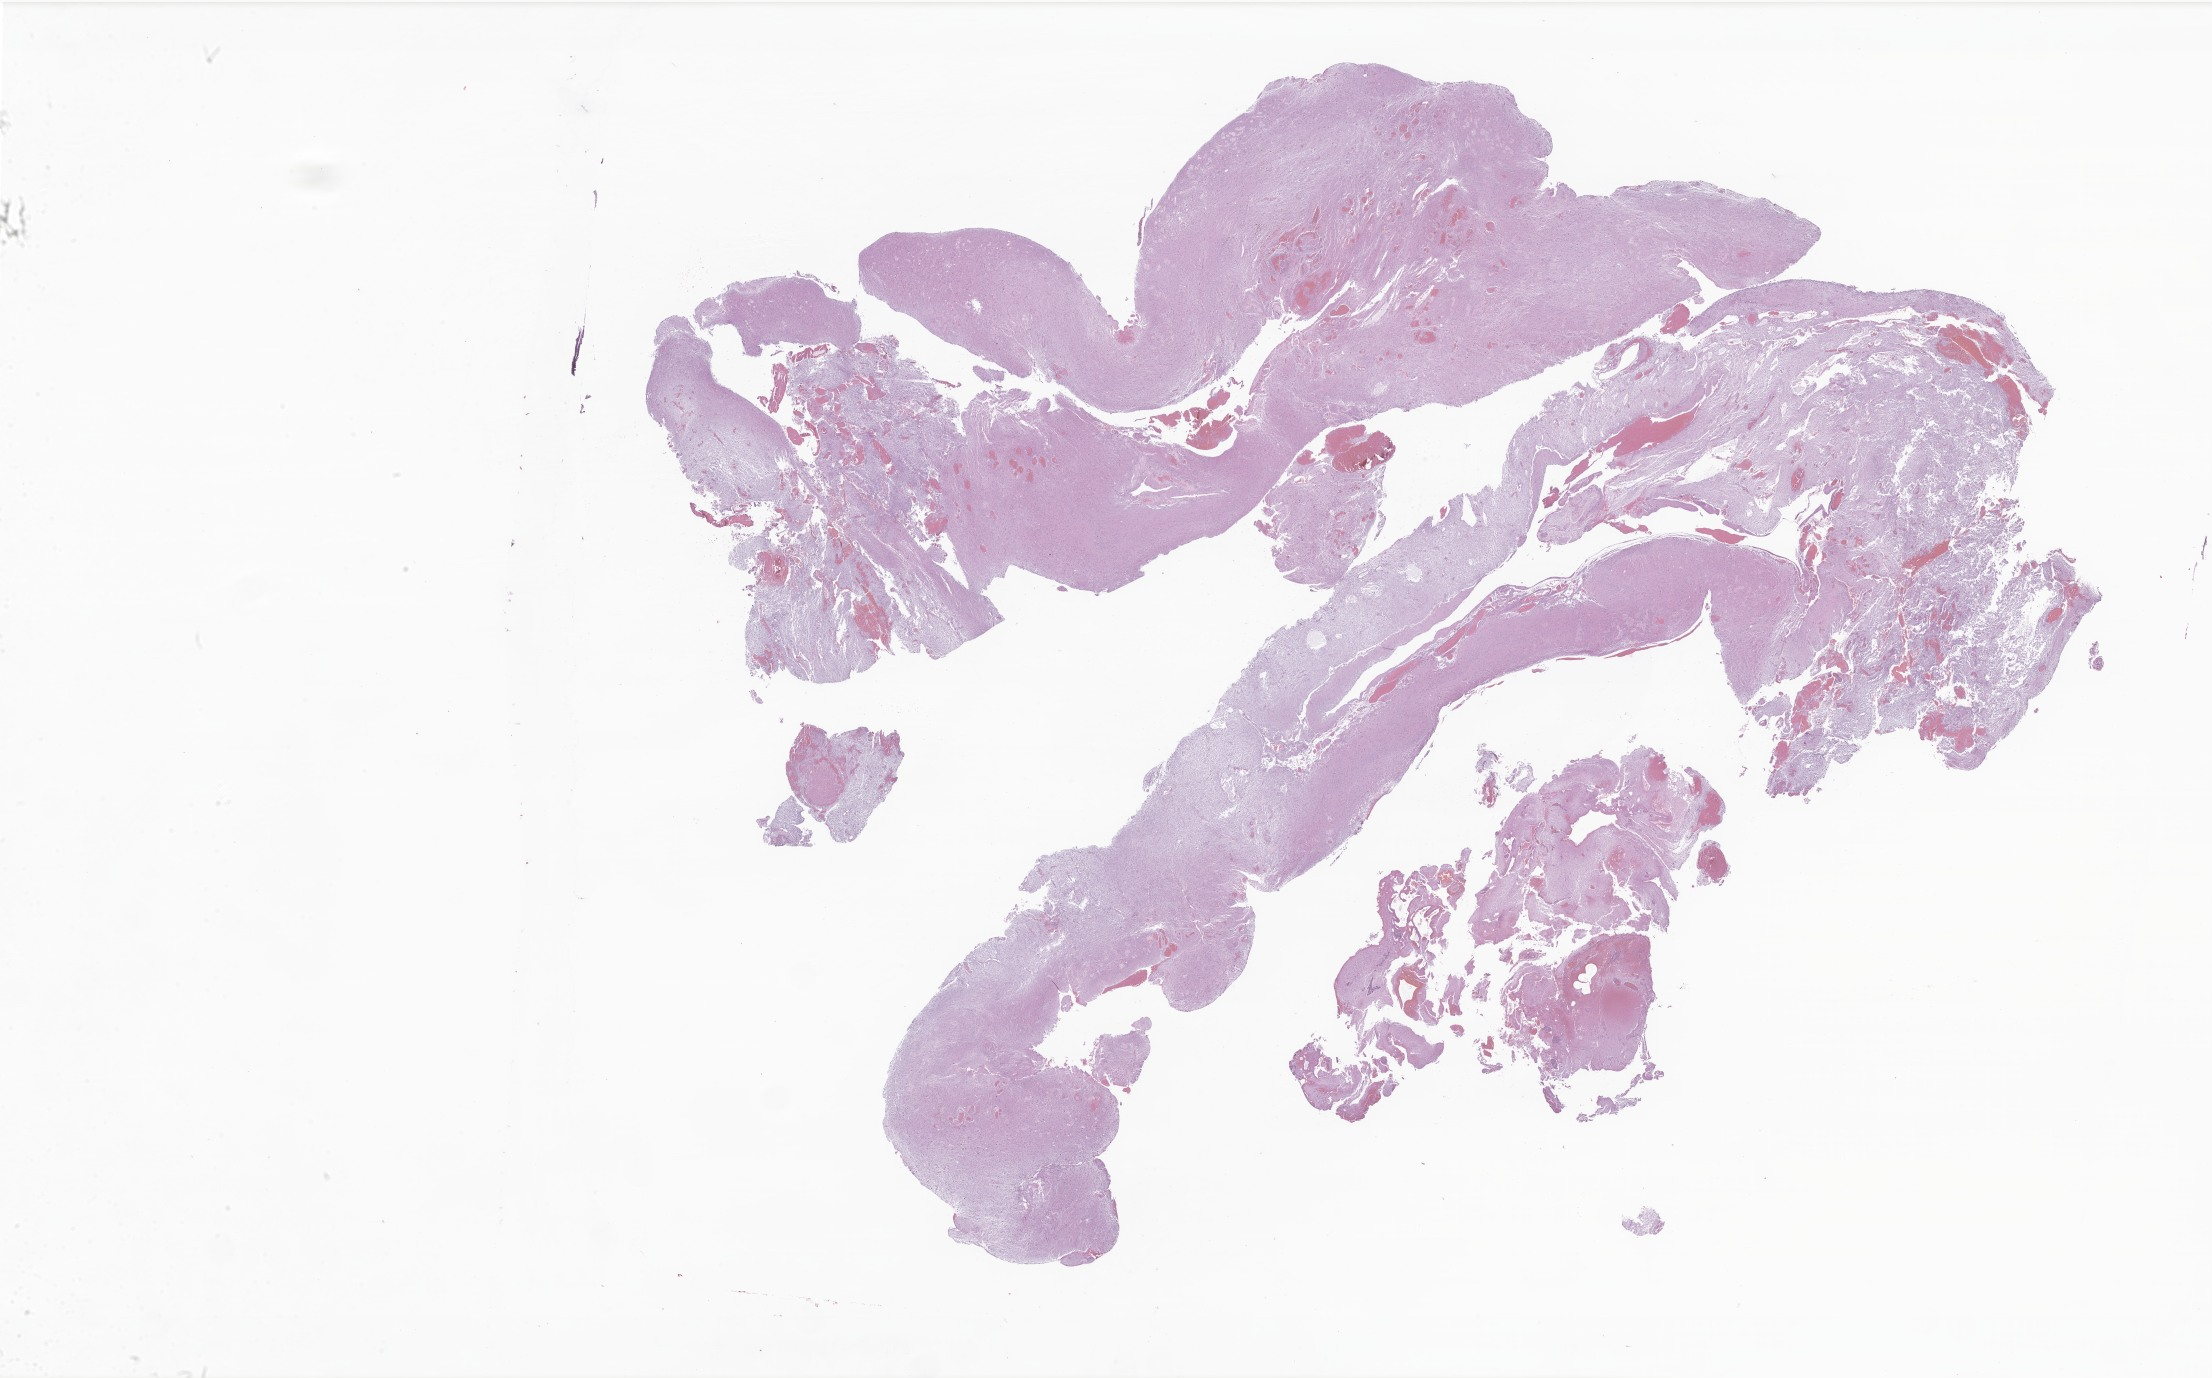
Digitized H&E-stained section of tumor tissue from the brain, low-resolution overview of the scanned area, about 37.3 x 23.2 mm. Formalin-fixed paraffin-embedded section. Male patient, age 97 months.
Diagnosis (ICD-O-3 morphology term): Pilocytic astrocytoma.